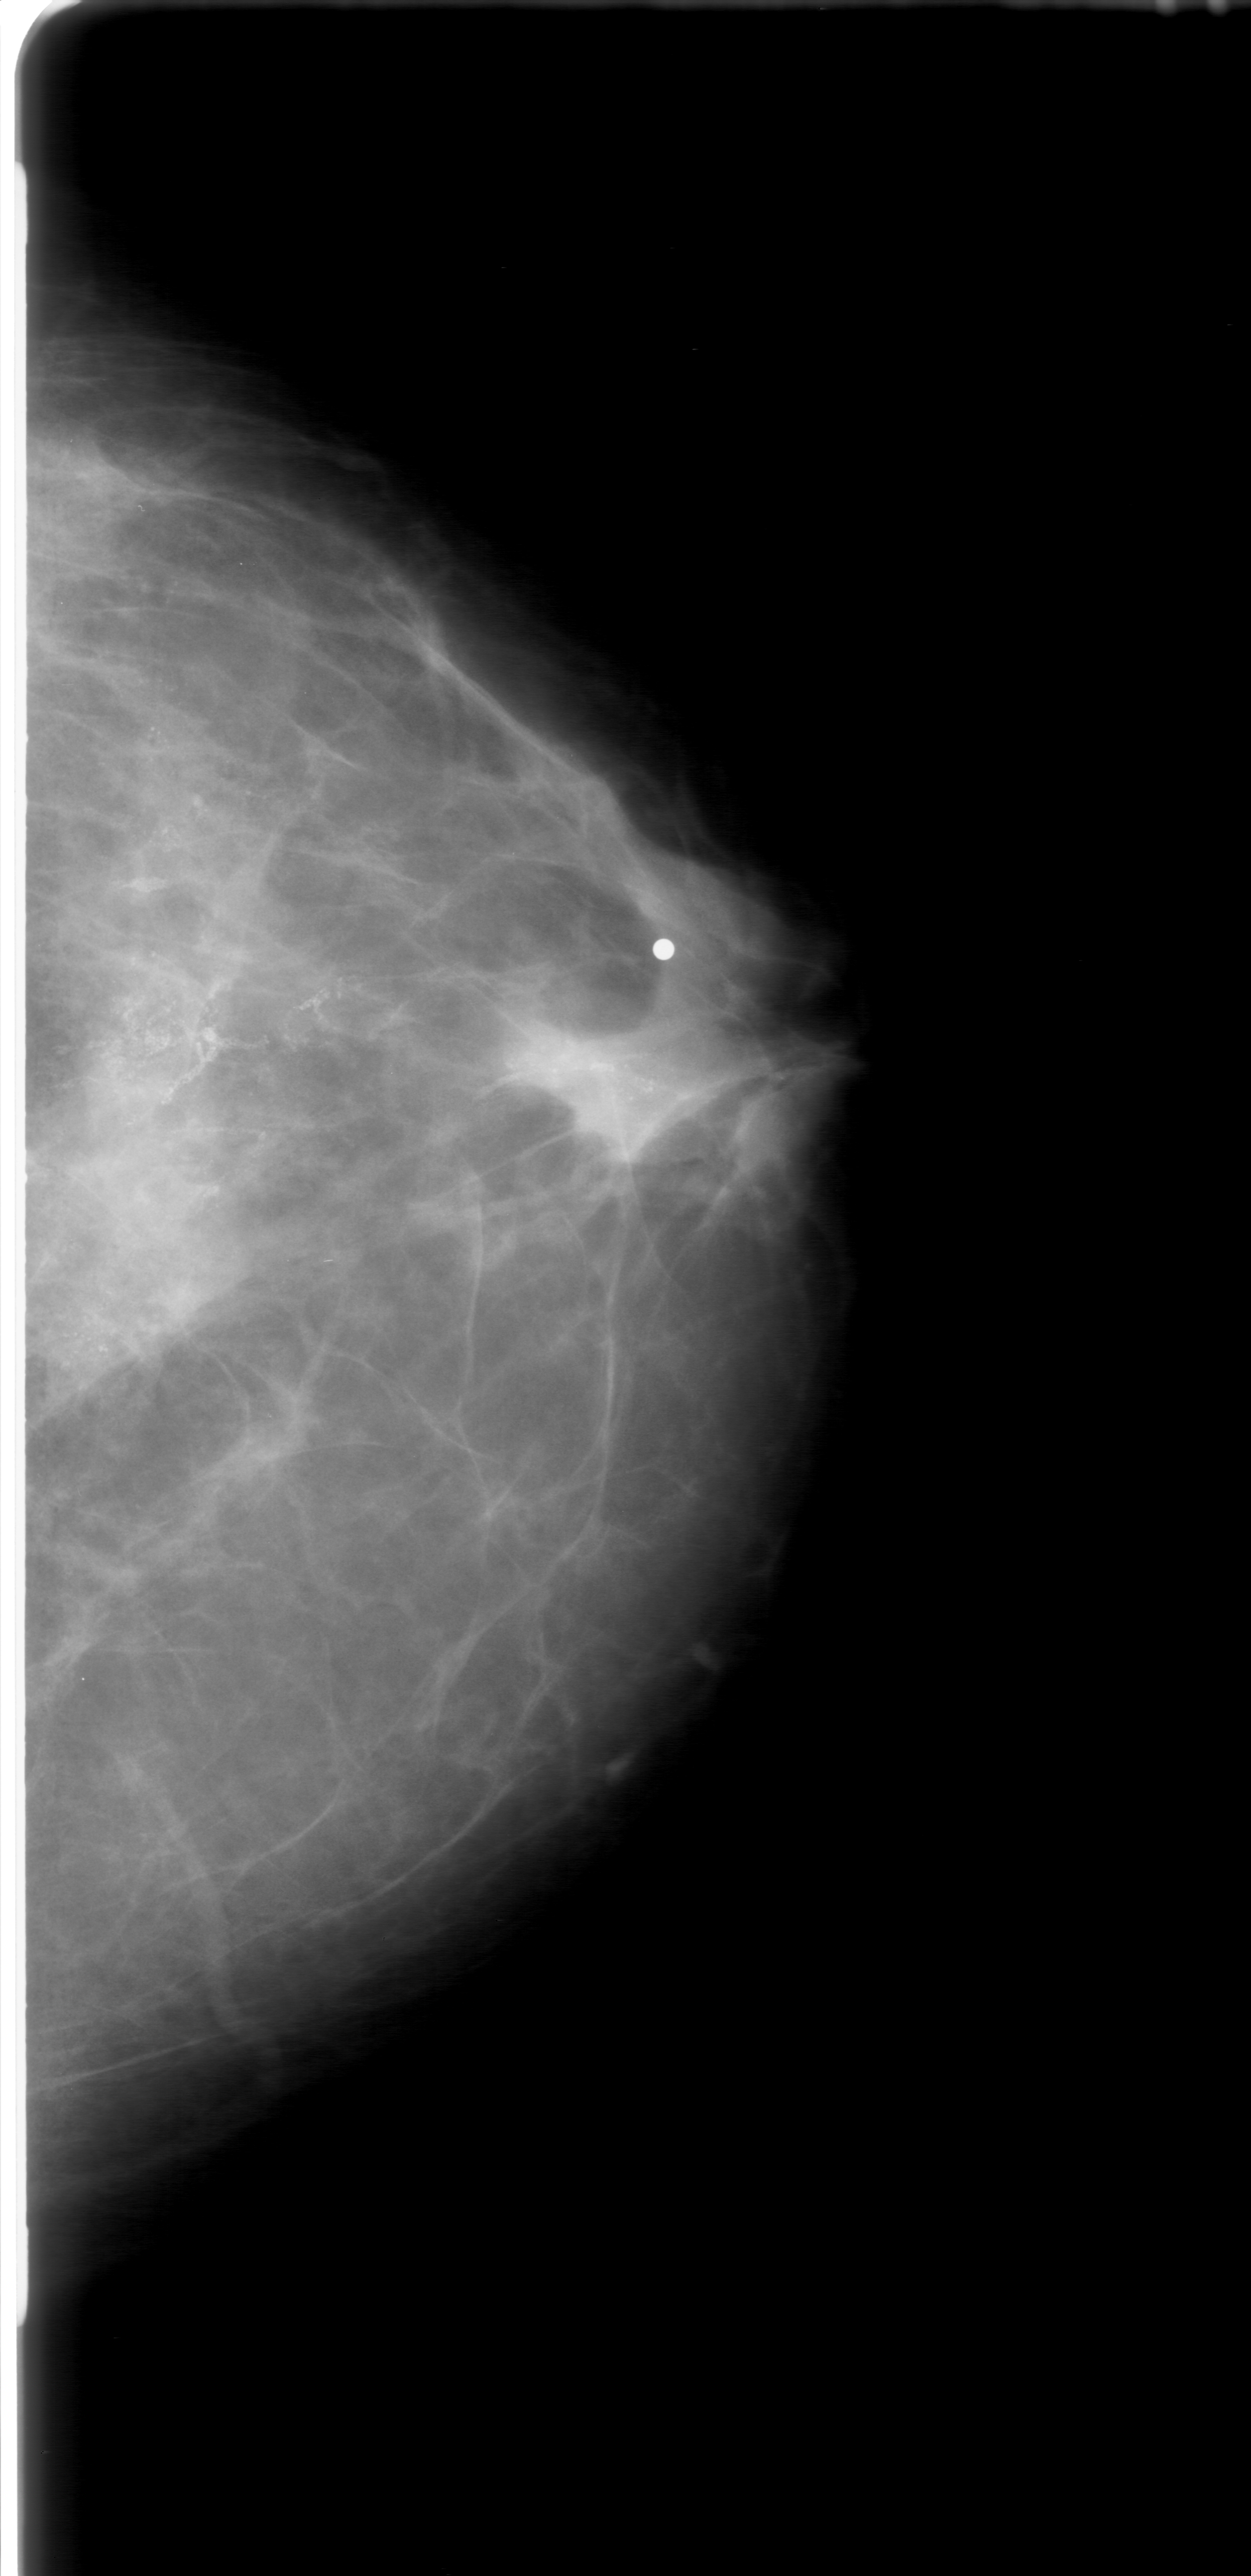
Mammogram (digitized film), left breast, craniocaudal (CC) view.
Abnormality record for this image: calcifications, morphology amorphous, distribution linear; BI-RADS assessment category 5; subtlety rating 5 on a 1 (subtle) to 5 (obvious) scale; pathology (as recorded): malignant.